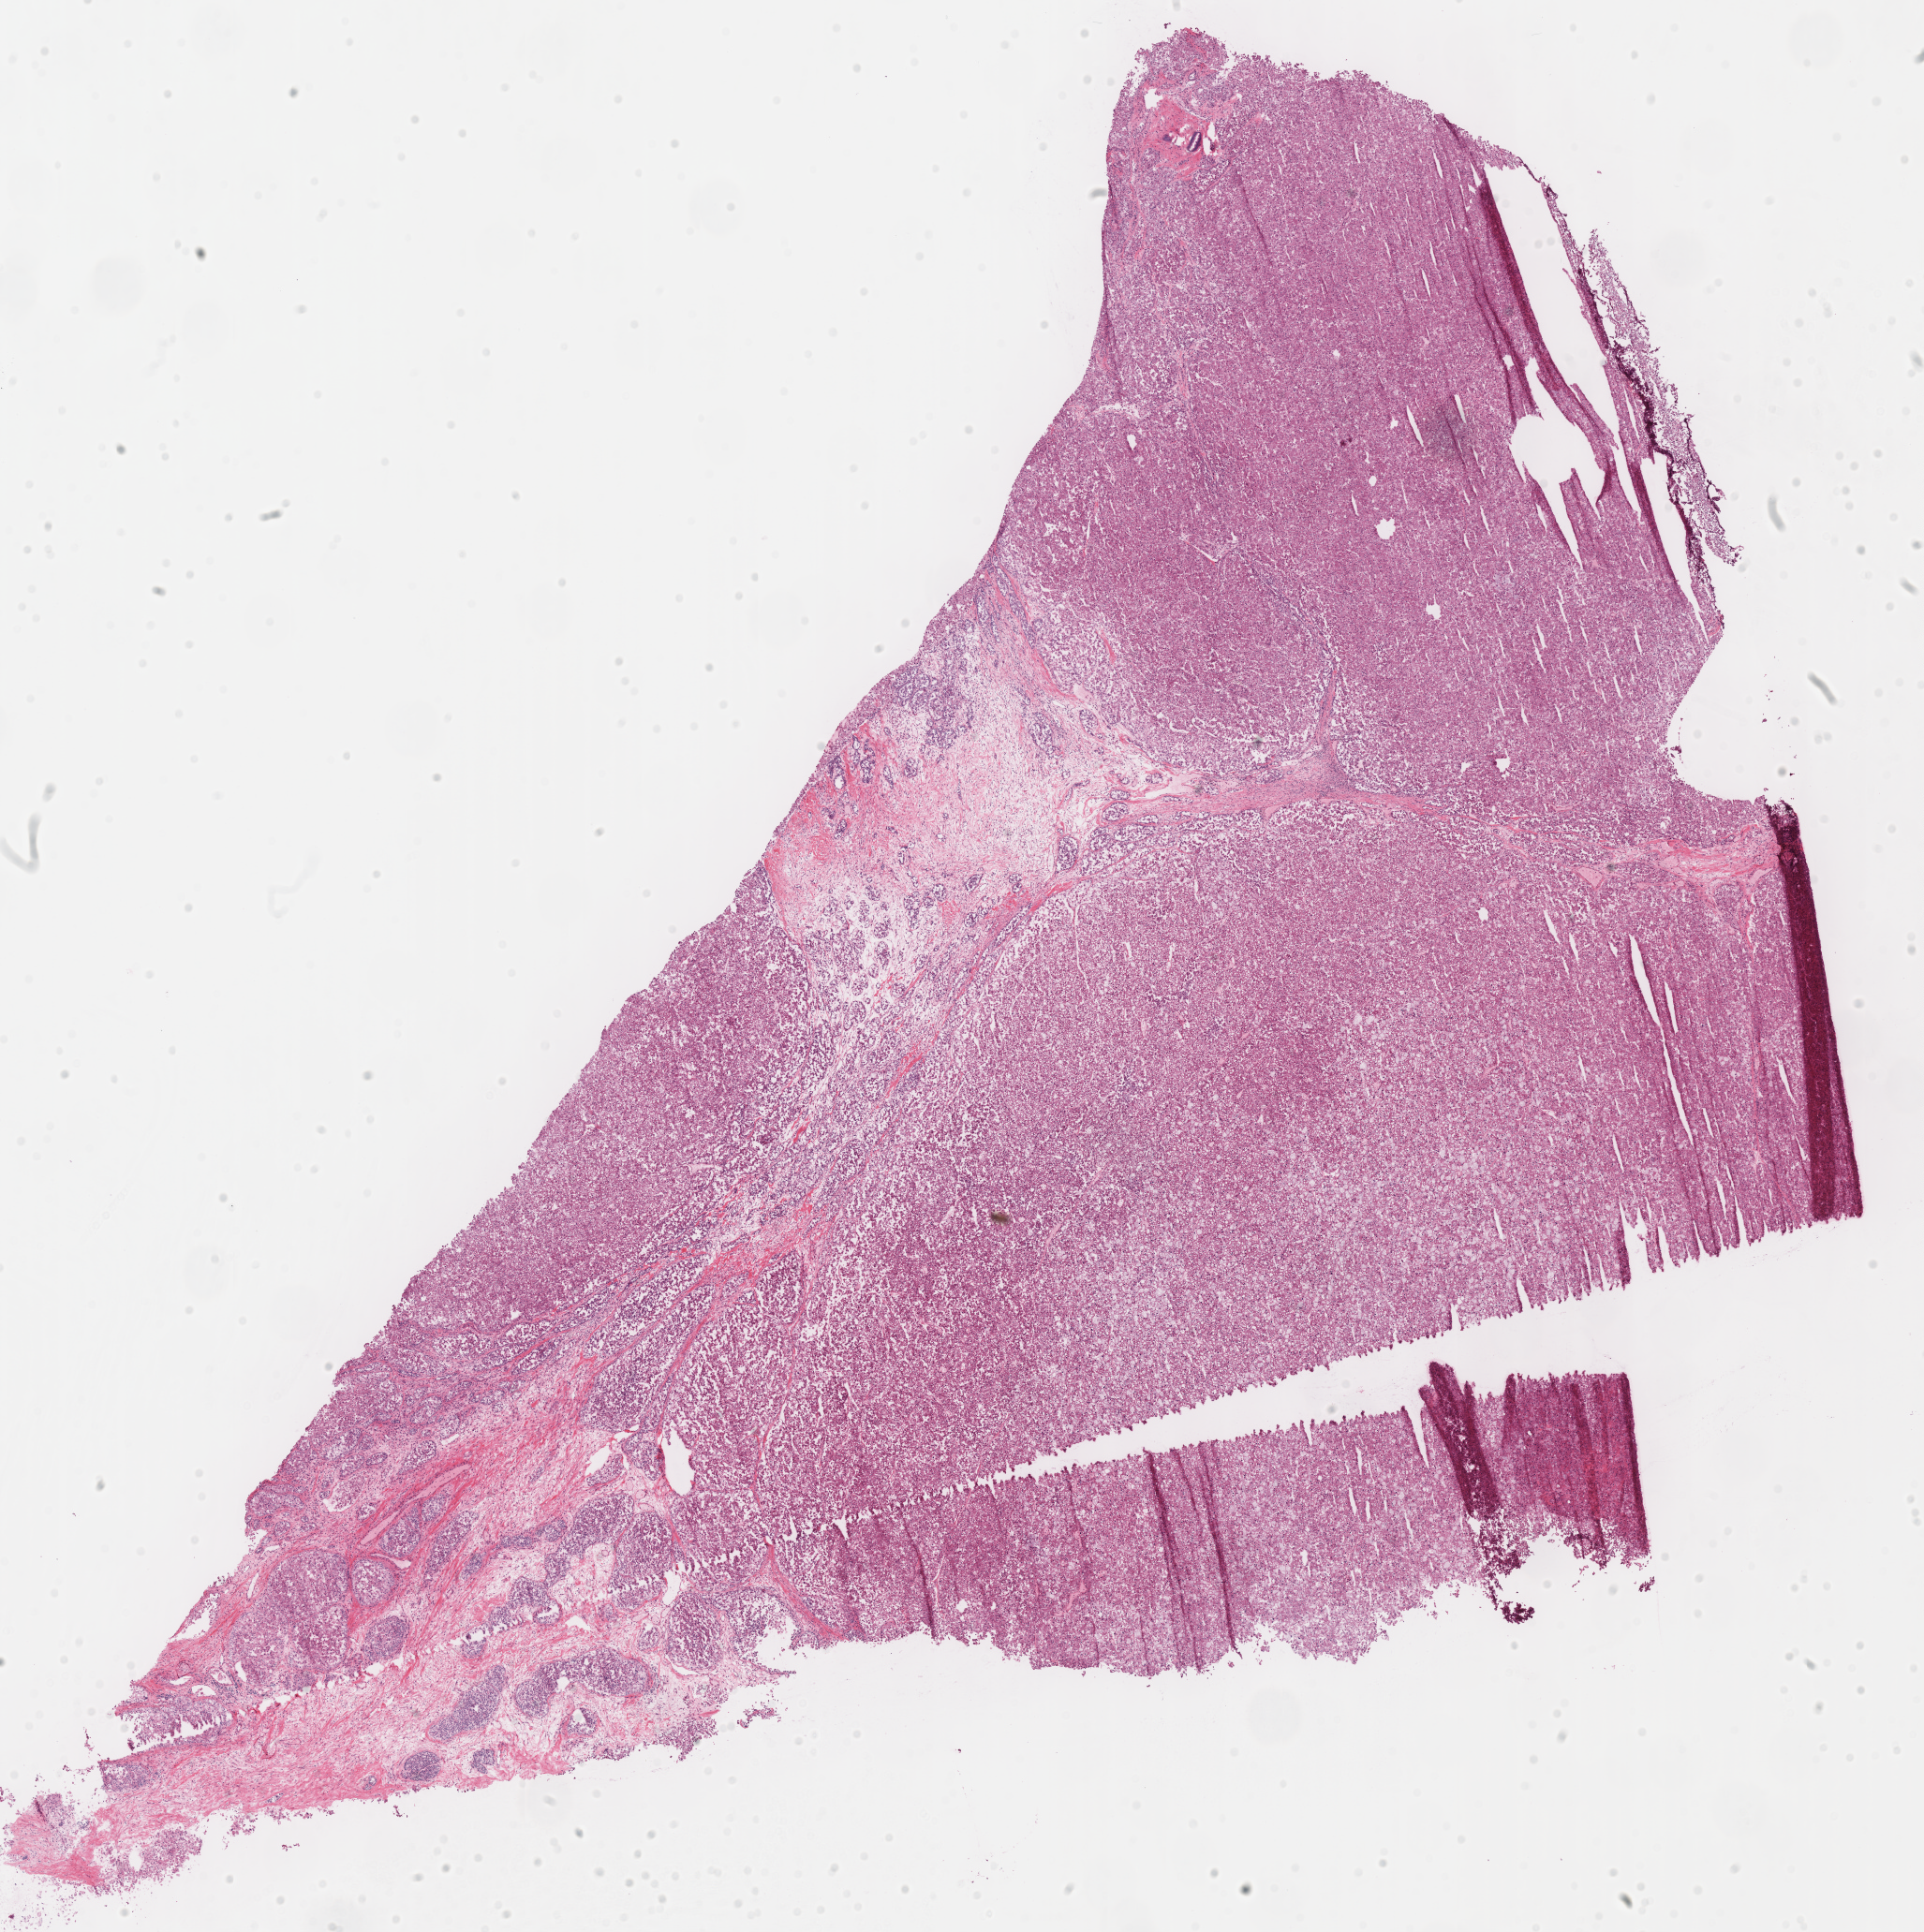
Whole-slide histology image, H&E-stained — low-resolution overview of the scanned area, about 16.2 x 16.2 mm, frozen section from the top of the tissue portion, primary tumour sample from the kidney. Patient: male, age at initial diagnosis 67 years. Slide review estimates, as recorded: tumour cells 90%, tumour nuclei 90%, normal cells 0%, stromal cells 10%, necrosis 0%. Infiltration values recorded for this section: lymphocyte infiltration 2%, monocyte infiltration 0%, neutrophil infiltration 0%.
* AJCC pathologic stage: III (6th edition)
* laterality: left
* lymph nodes positive (case pathology): 0 of 8 examined
* pathologic diagnosis: Renal cell carcinoma, chromophobe type